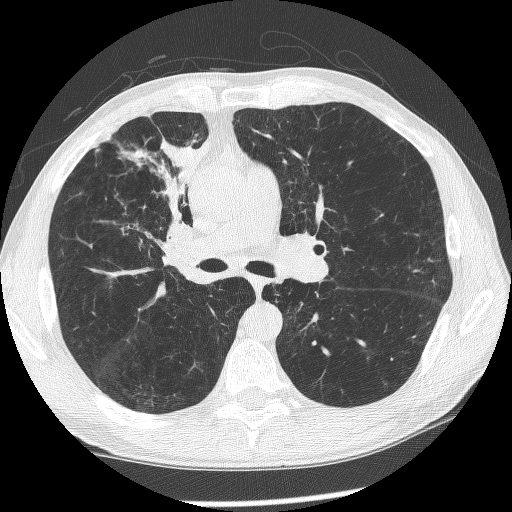
Low-dose screening chest CT, axial slice. First (baseline) screen. Lung window (W 1500 / L -600 HU). 1.25 mm slice thickness. Lung (sharp) reconstruction kernel (BONE). 512 × 512 image matrix, field of view 340 × 340 mm. Male participant, aged 60 years at enrolment. Current smoker at enrolment.
Expert reader's lesion annotation, bounding box [x1, y1, x2, y2] px = [145, 190, 220, 283]. The exam's reader record, not a measurement of the box and not confirmed to be the same lesion: non-calcified nodule or mass ≥4 mm, right upper lobe, 12 × 8 mm, spiculated (stellate) margins, mixed attenuation.